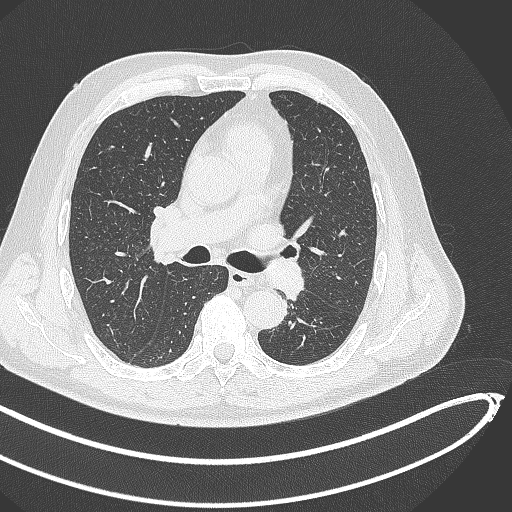
Chest CT, one axial slice. Position 276 of 468 along the scan axis. Reconstruction kernel B70f. 120 kVp. Lung window (W 1500 / L -600 HU). 1 mm slice thickness. 512 × 512 image matrix, field of view 400 × 400 mm. Patient: male, 64 years. Case-level facts recorded for this patient, not image findings: clinical TNM (as recorded): T1c N0 M0; histopathological grade: G2.
Outlined on this slice (rectangle marked by the reading radiologist):
- lung tumour (recorded histology: squamous cell carcinoma): bounding box [x1, y1, x2, y2] px = [270, 257, 307, 303]